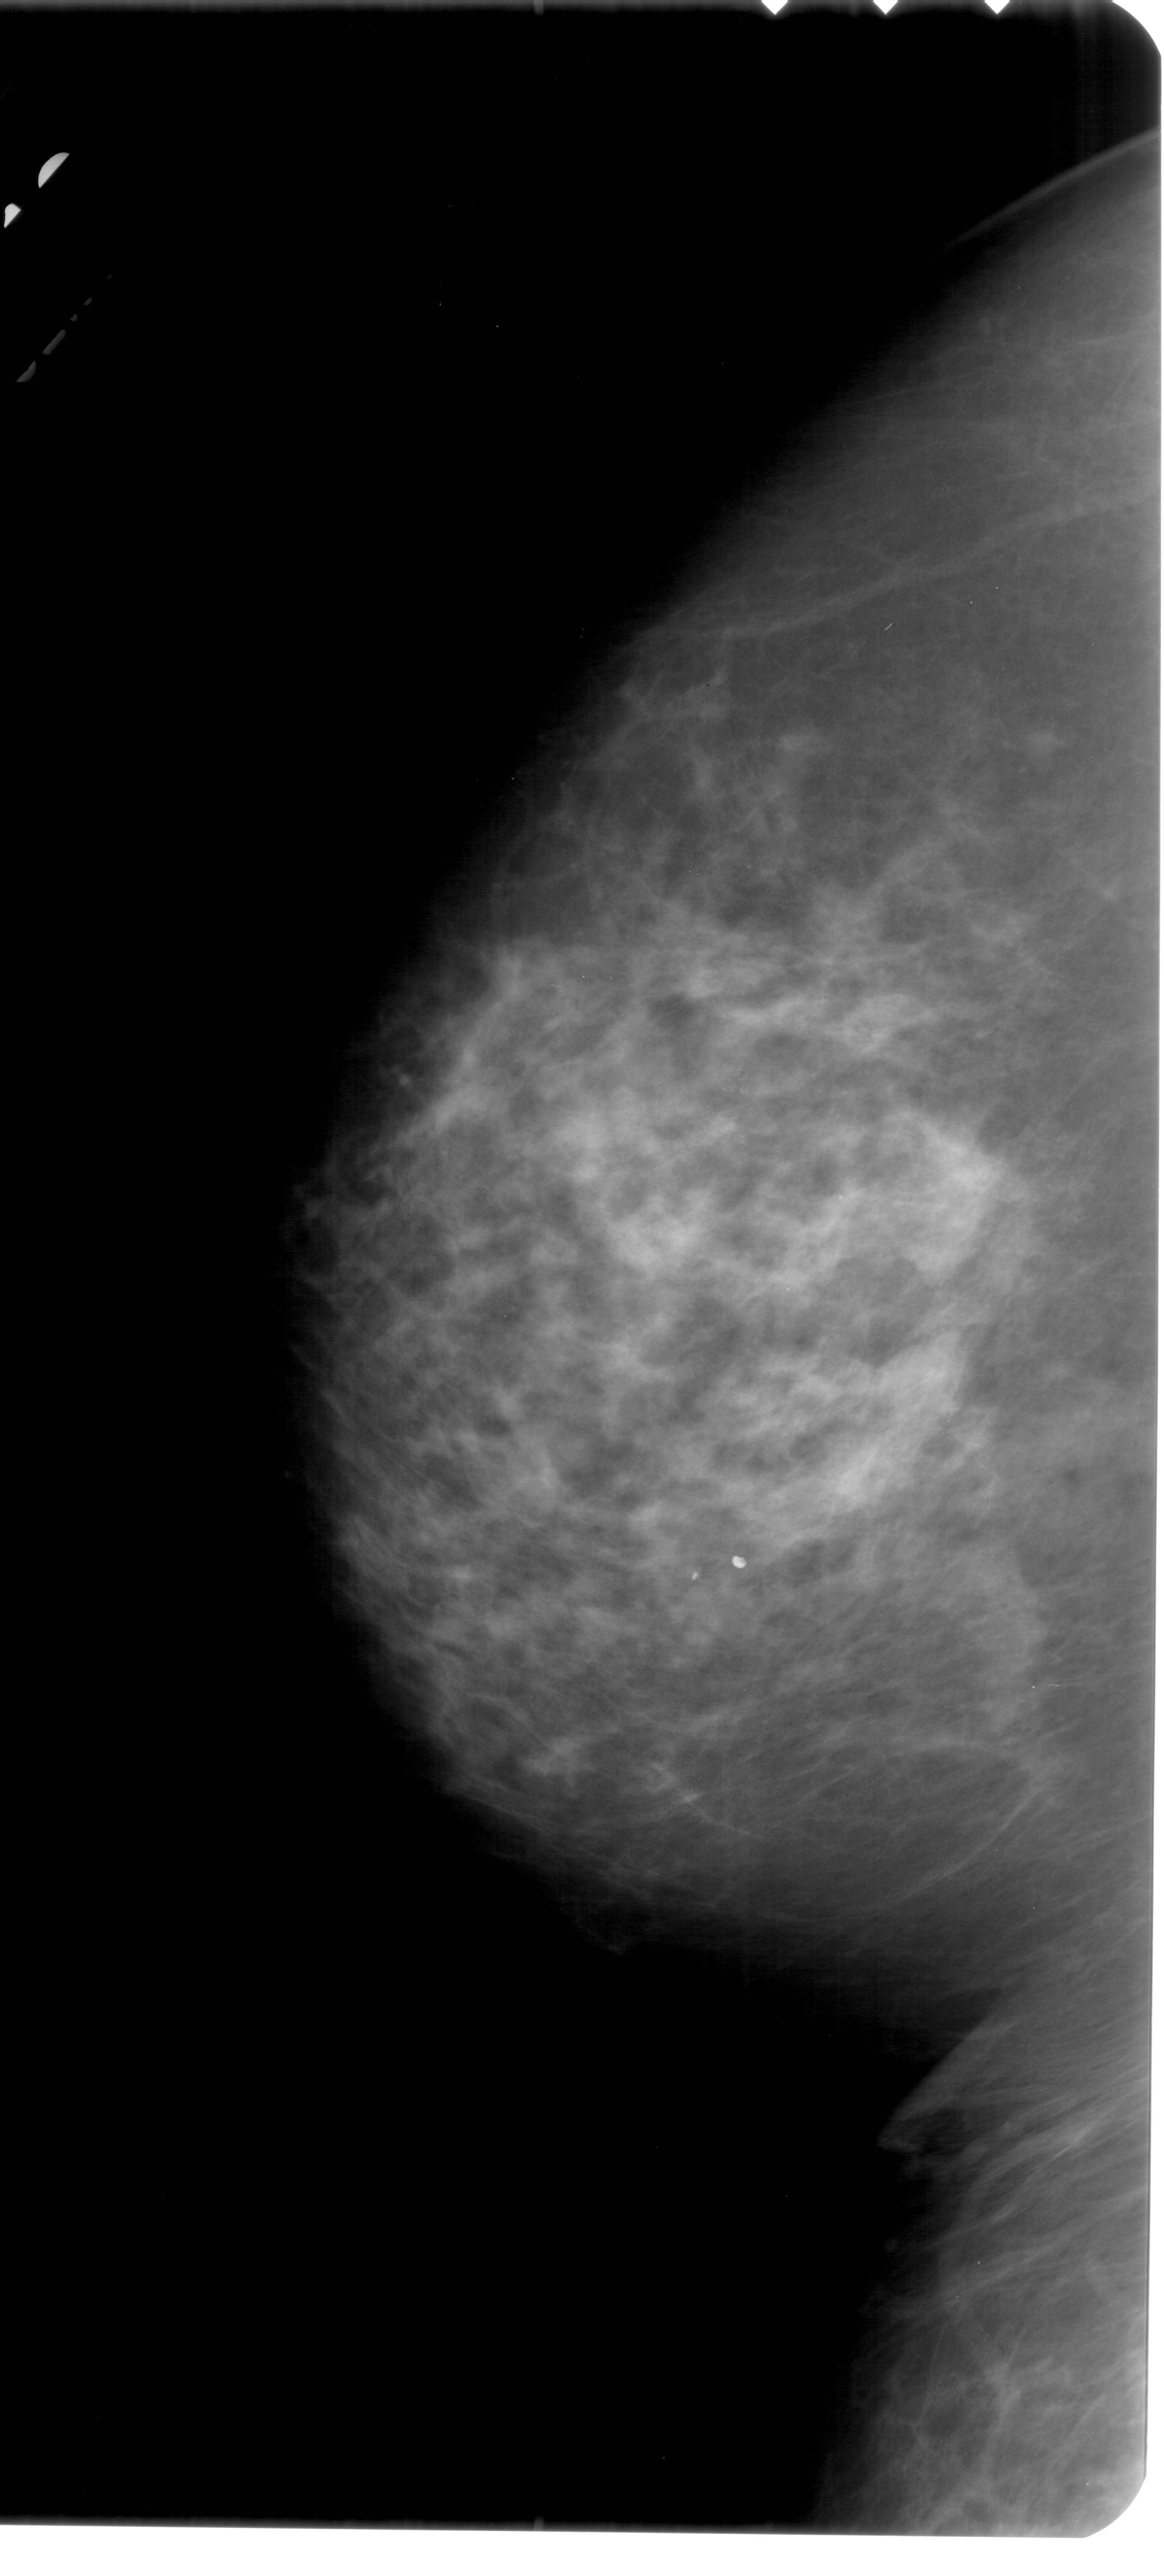
Digitized screen-film mammogram; left breast; craniocaudal (CC) view; BI-RADS breast density category 3 (scale 1–4).
Marked findings (only marked abnormalities are described; nothing is implied about the rest of the image): calcifications, morphology pleomorphic, distribution clustered; BI-RADS assessment category 4; pathology result (as recorded, not read from the image): malignant.